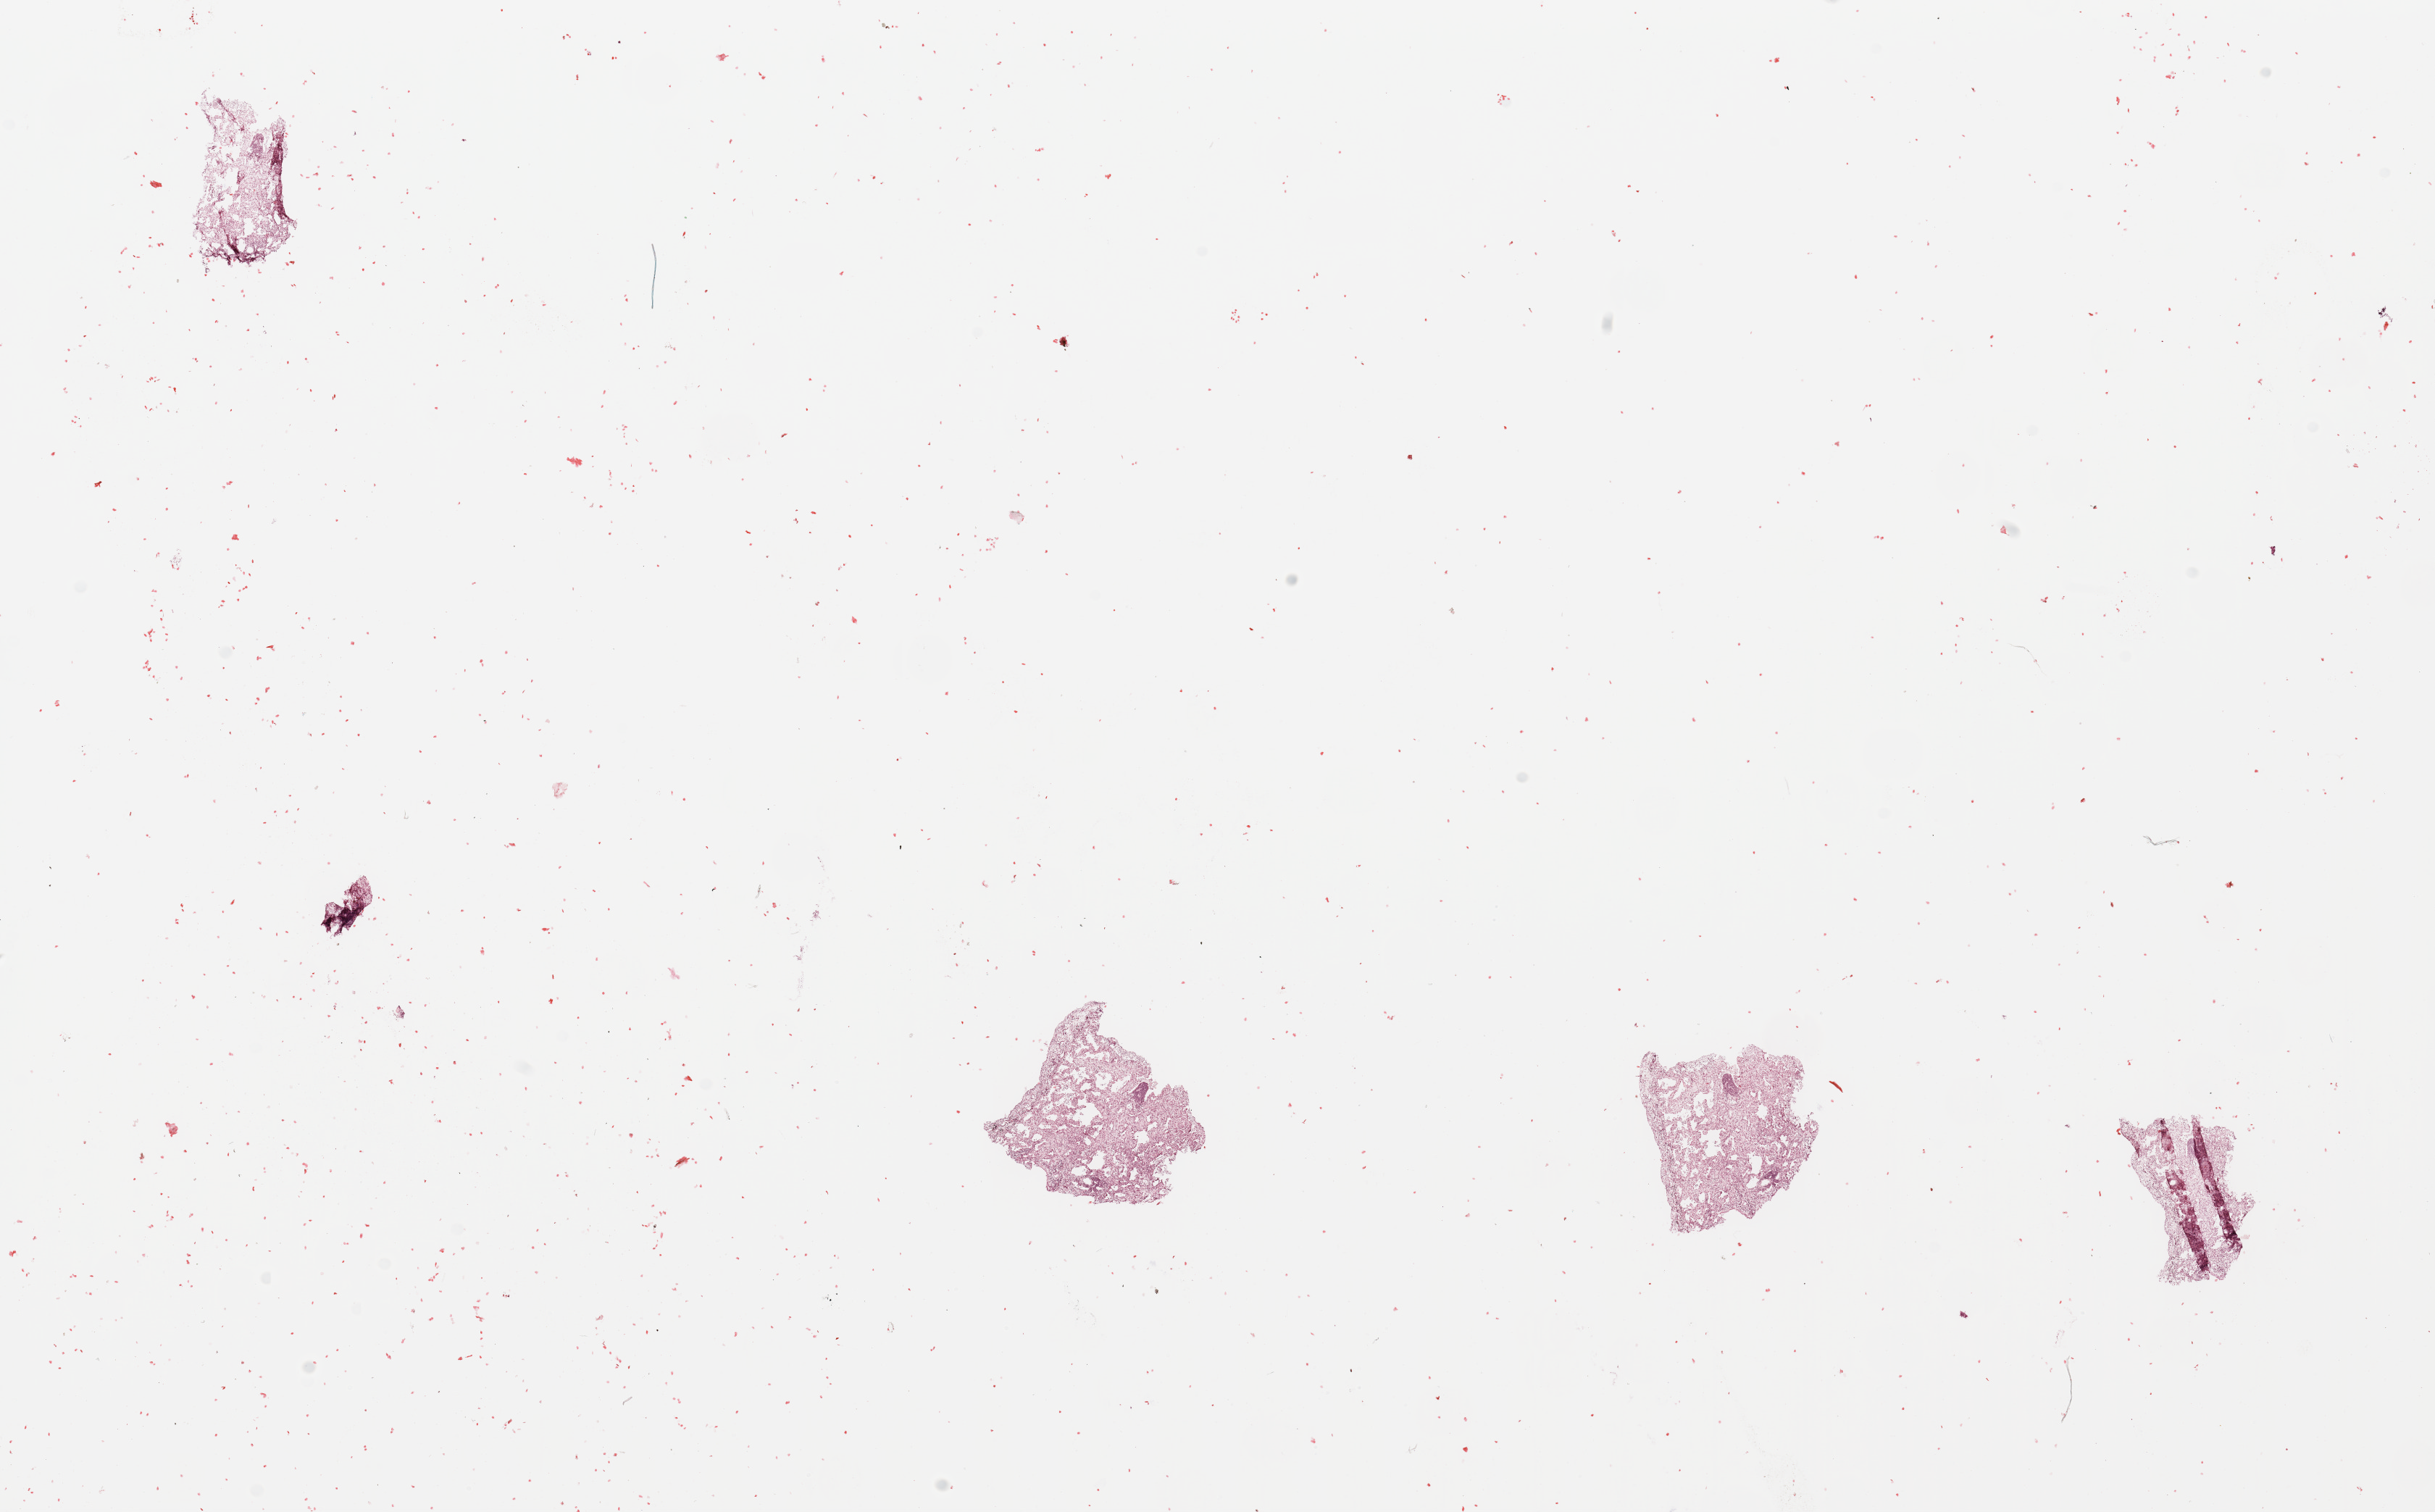
H&E whole-slide image — a low-resolution overview of the entire scanned area, about 26.6 x 16.5 mm (from a 20x scan), normal (non-tumour) tissue sample, sampled site: lung. 69-year-old female patient.
This section: normal (non-tumour) tissue from the same patient. Patient diagnosis: Squamous cell carcinoma, NOS.